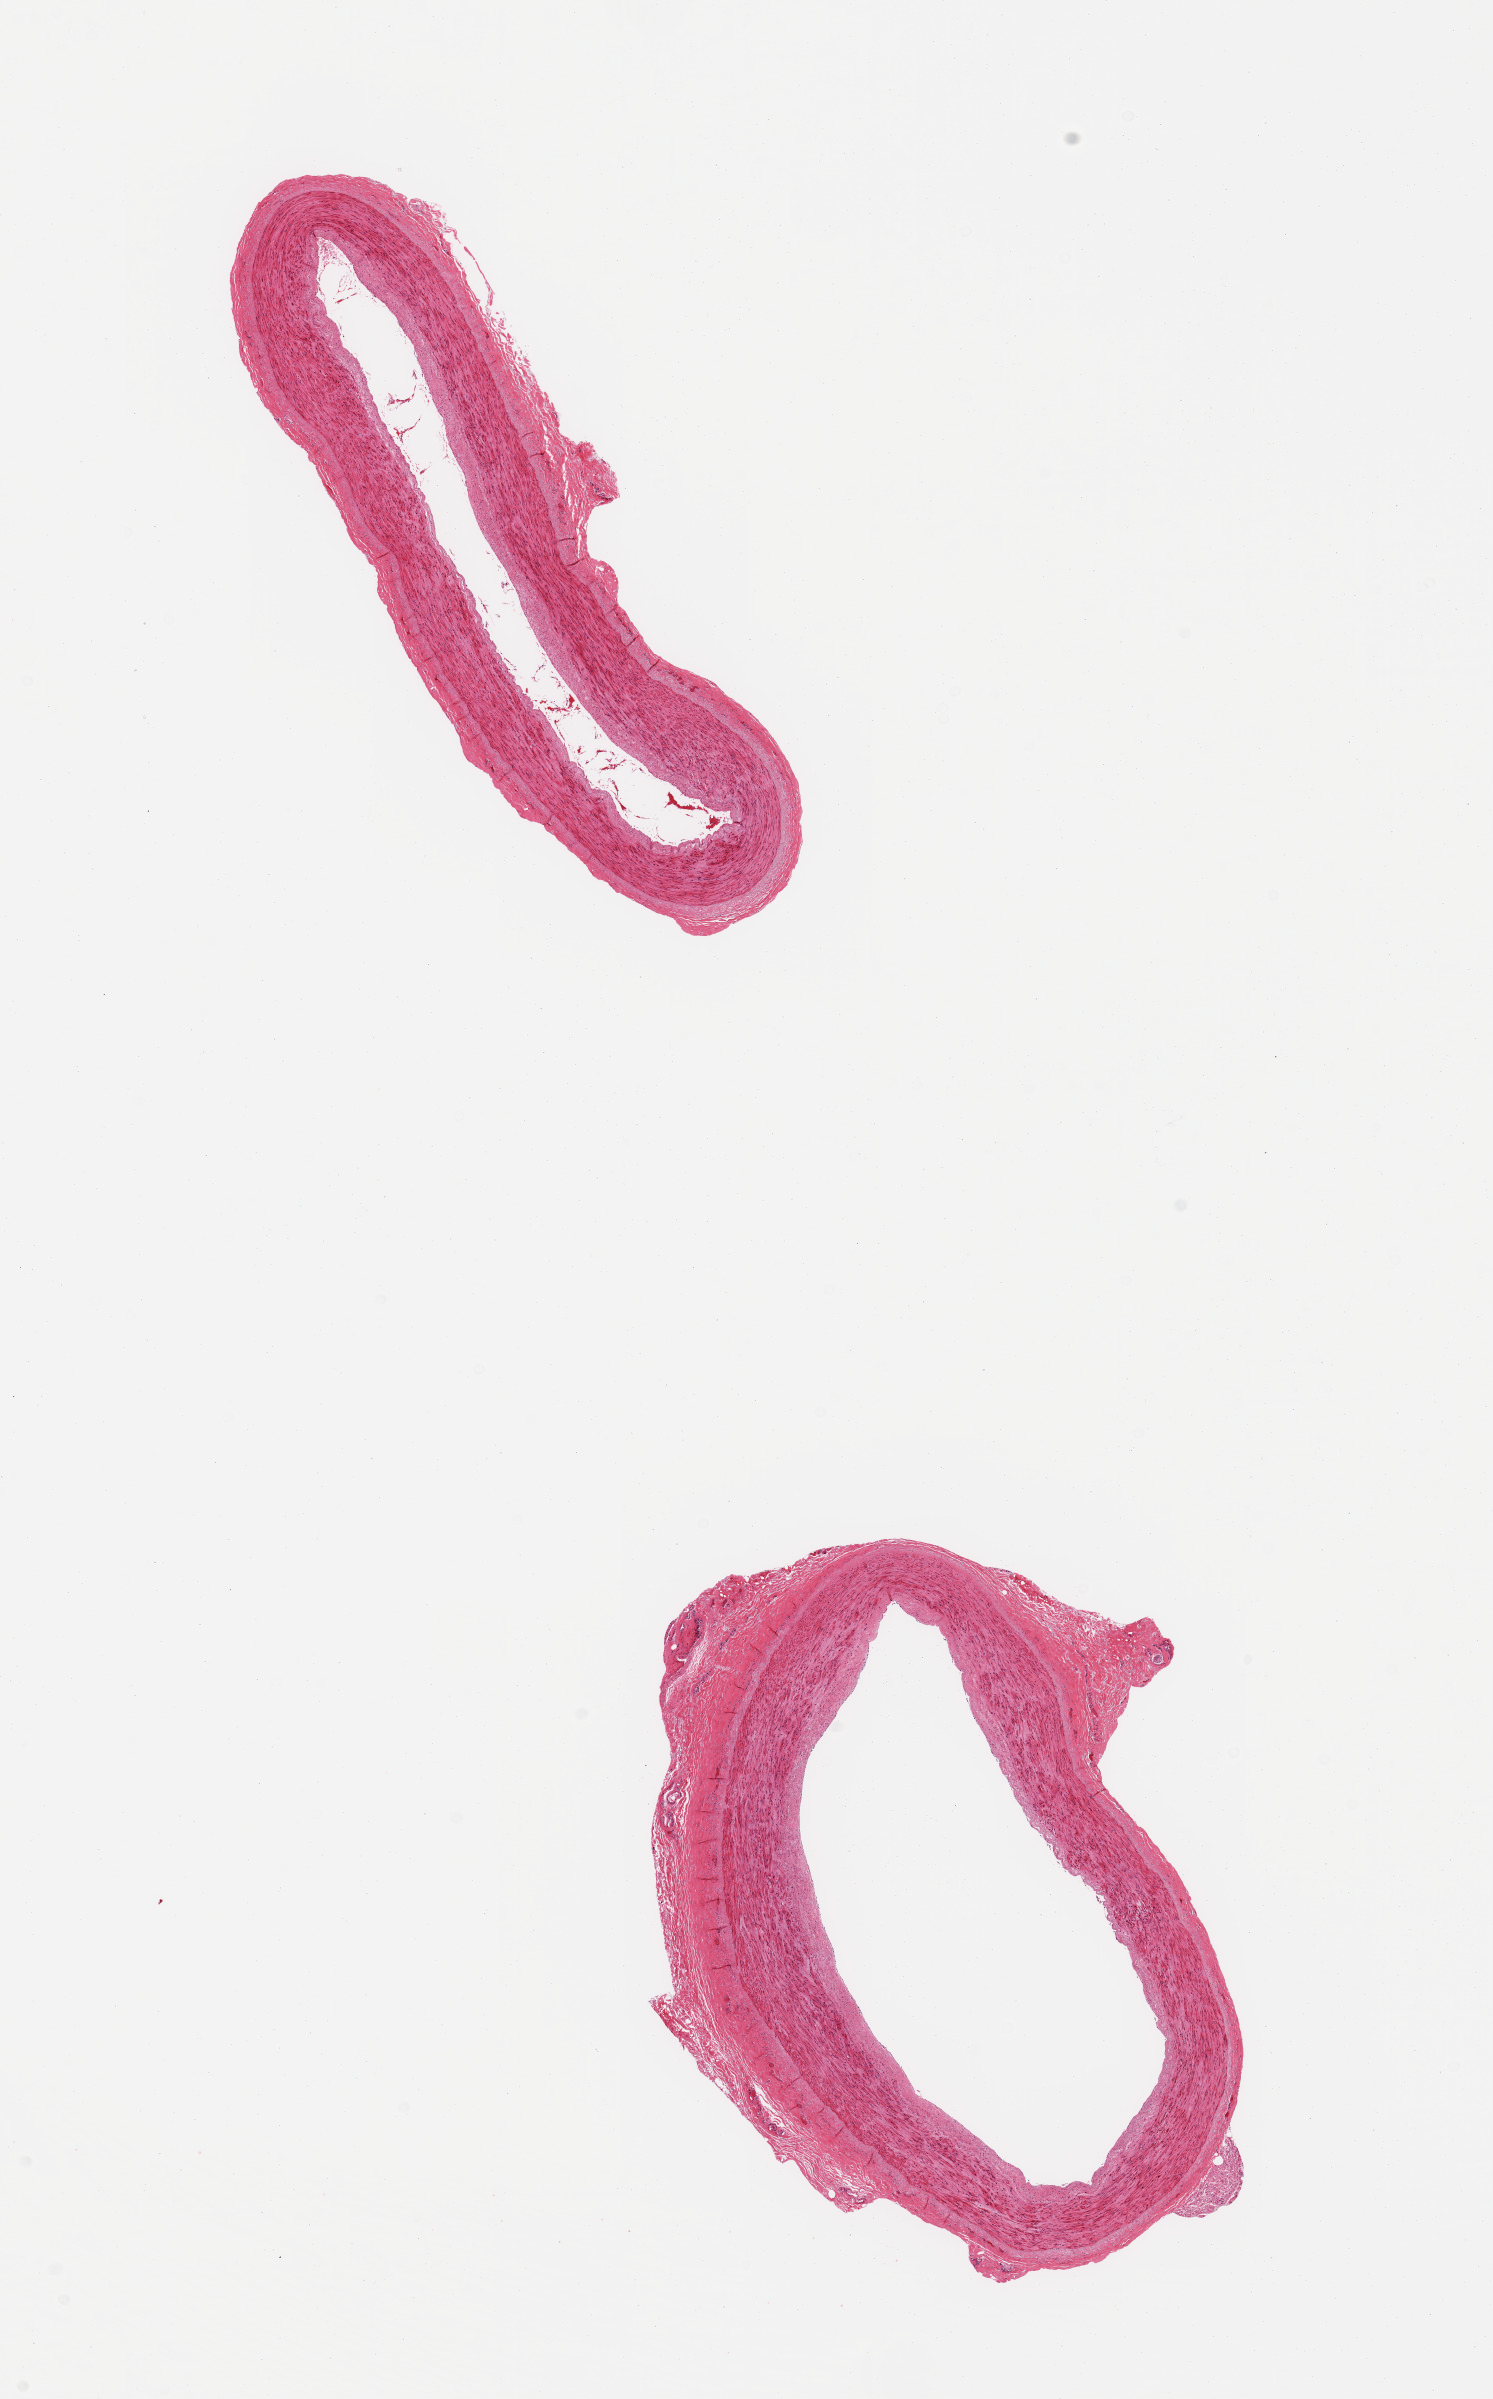
Whole-slide image, haematoxylin and eosin stain — whole scanned area (about 11.8 x 19.0 mm) shown as a low-resolution overview. PAXgene-fixed paraffin-embedded (PFPE) section. Target tissue: tibial artery. Tissue donor sample. Donor: male.
- pathologist's review note for this sample: 2 pieces; lumina open; rim of adherent adventitia